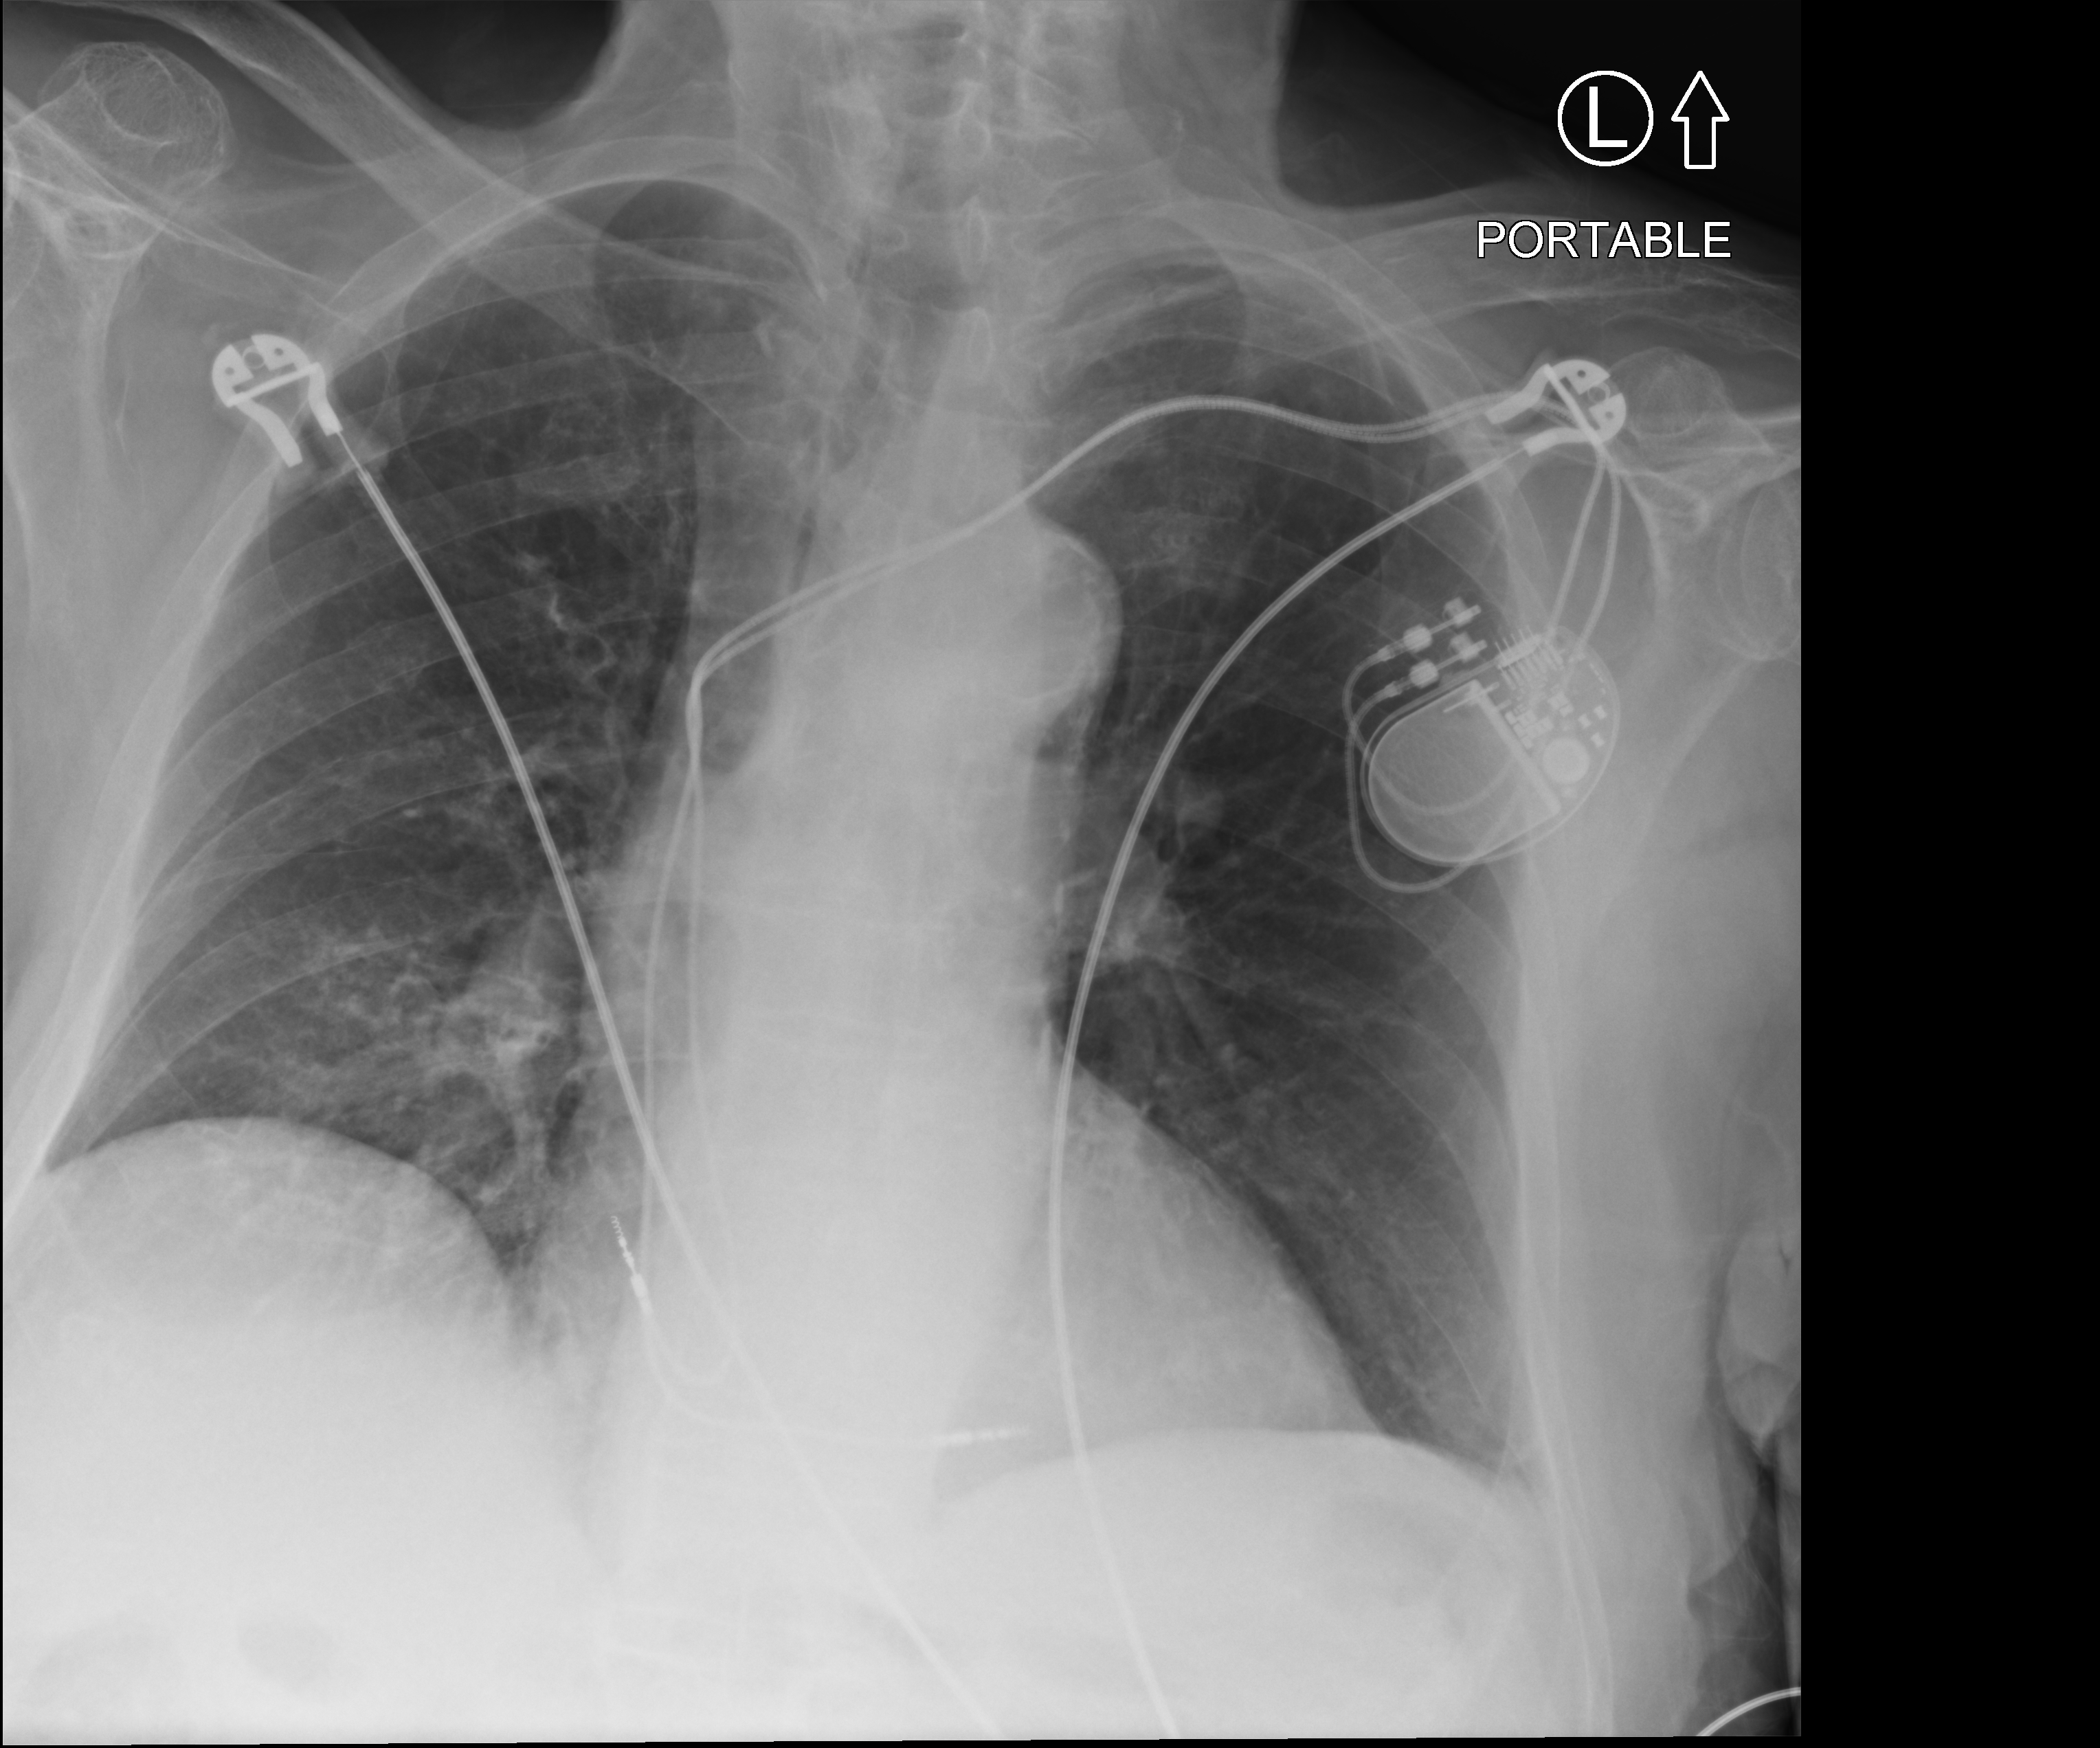
Portable chest radiograph; anteroposterior (AP) projection. Male patient hospitalised with COVID-19, age 75–90 years.
Admission-level facts for this patient (not findings on this image; timing relative to this image not recorded): admitted to intensive care during this hospital stay: no.